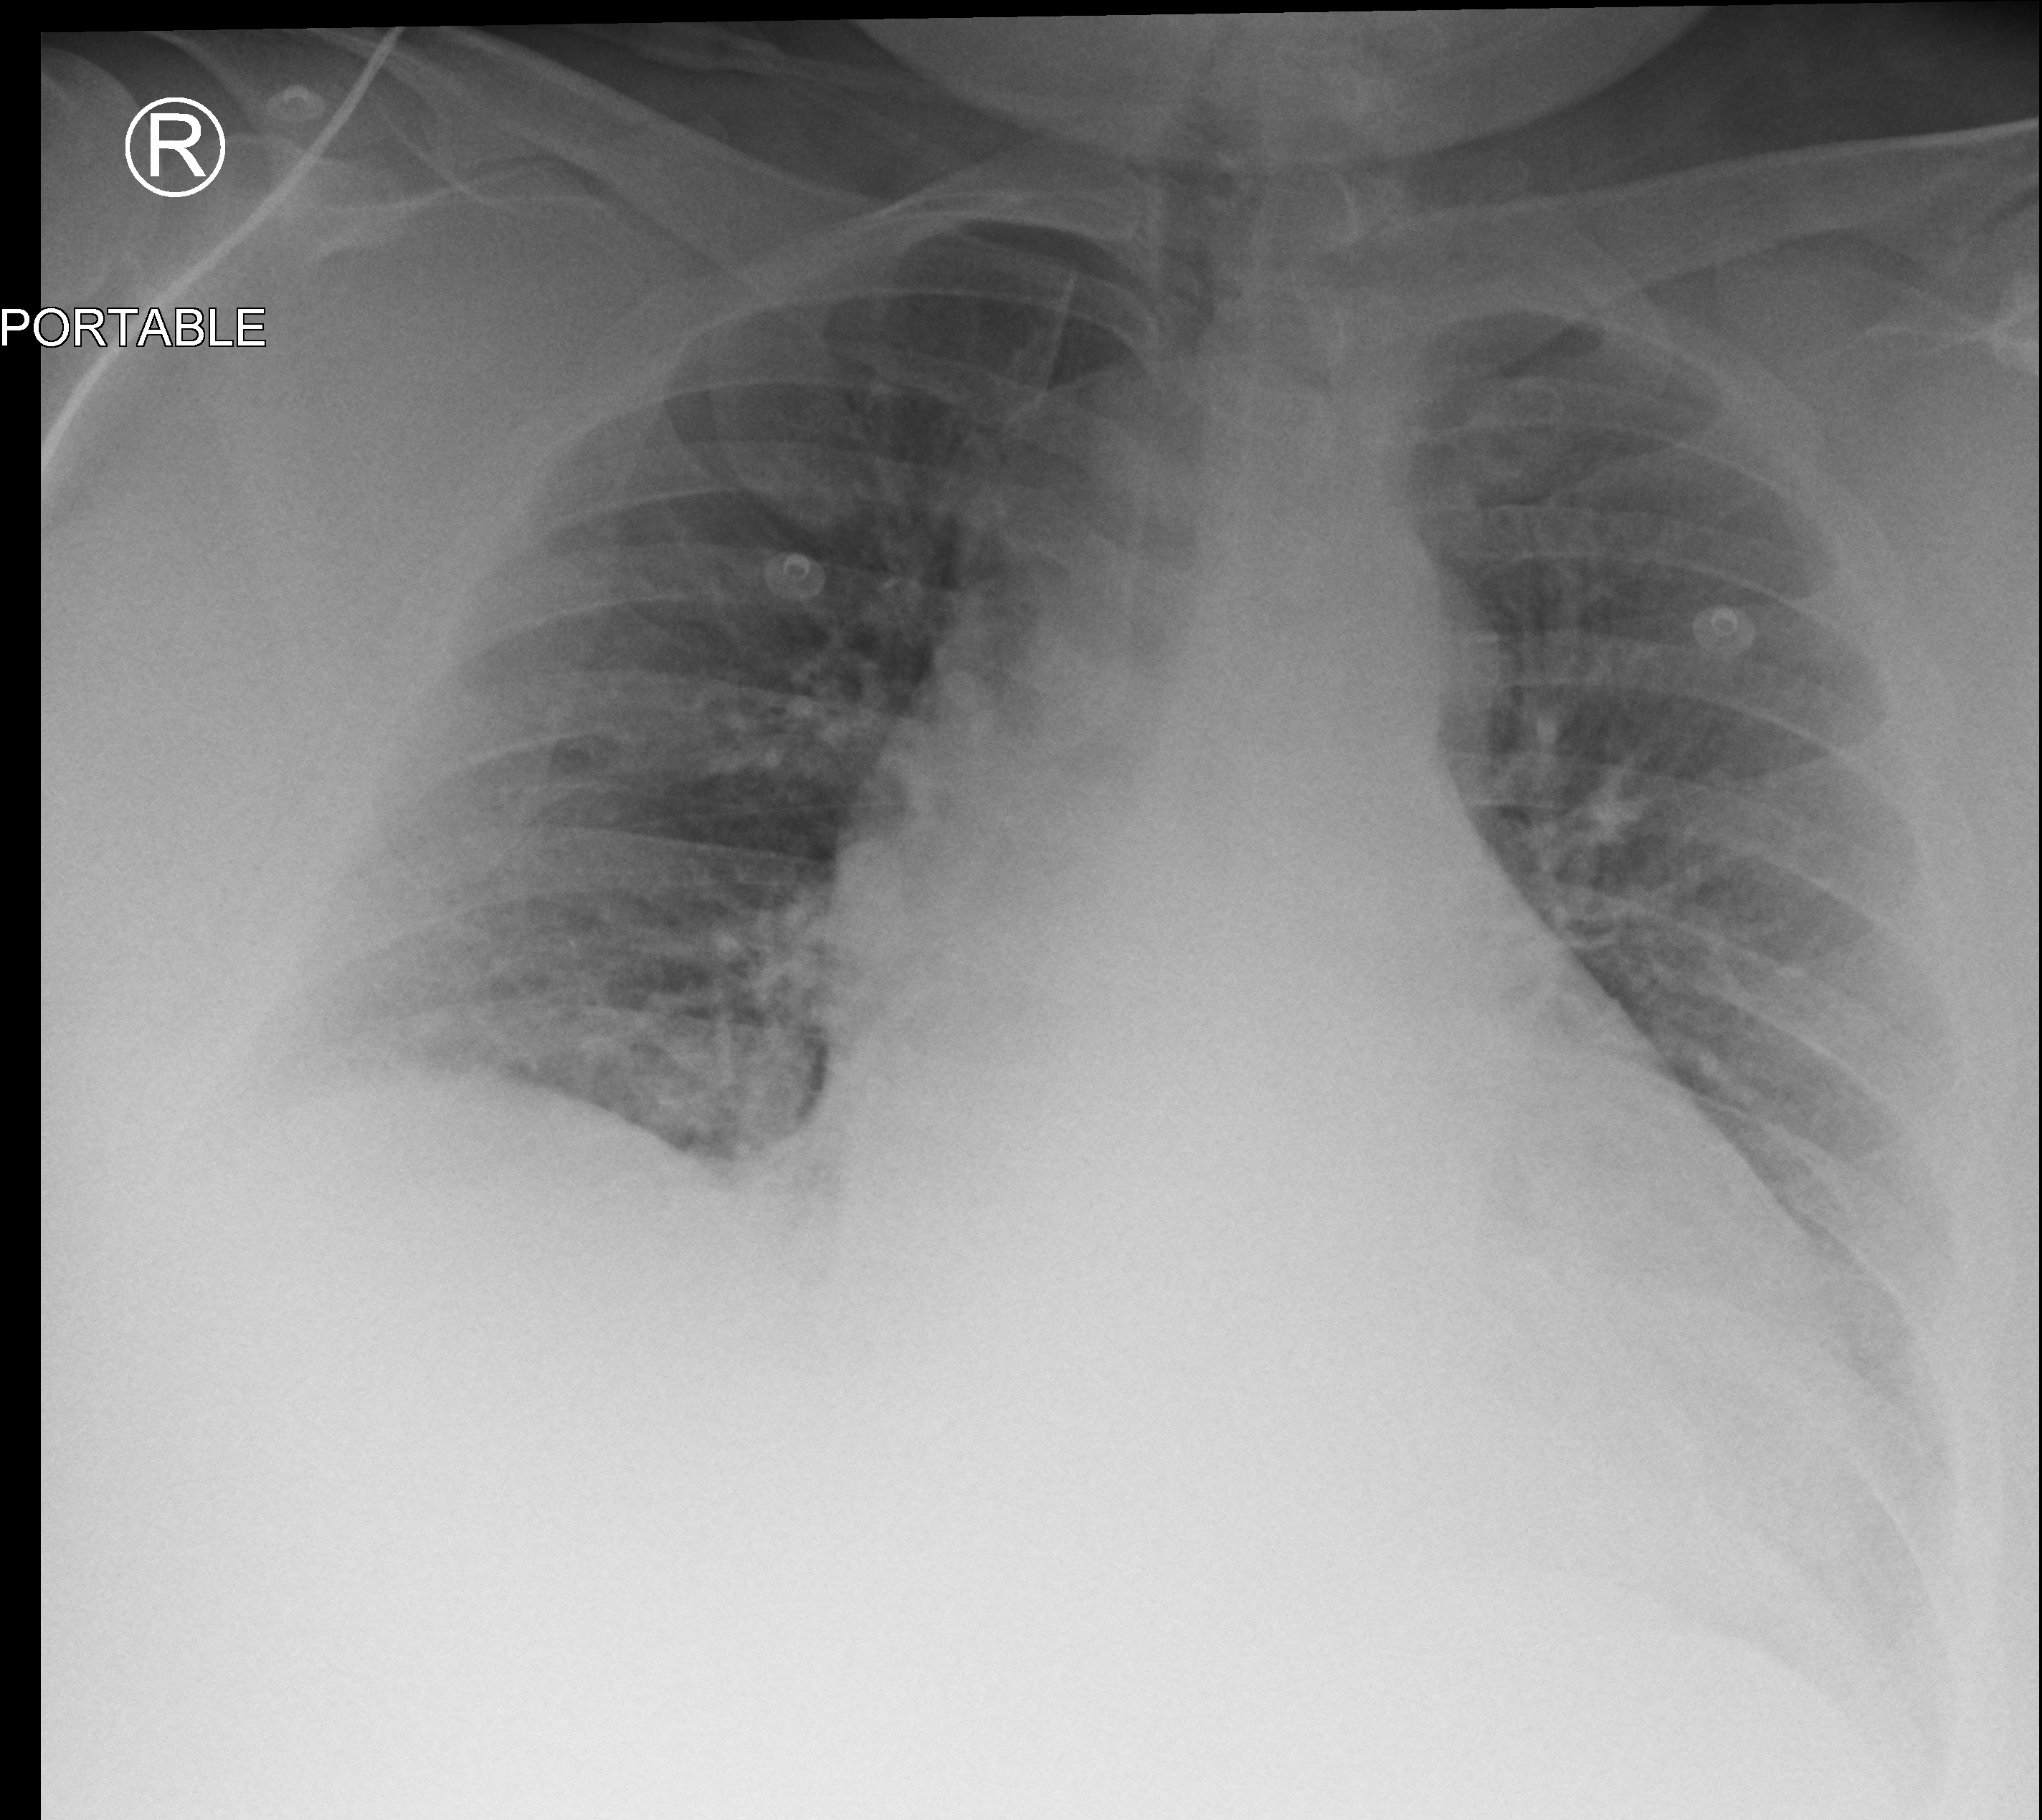
Bedside chest radiograph (computed radiography), anteroposterior (AP) projection. Patient hospitalised with COVID-19; male, aged 18–59 years.
Hospital-stay facts (about this admission, not read from this image; timing relative to this image not recorded): COPD (admission record): no; admitted to intensive care during this hospital stay: no; mechanically ventilated during this hospital stay: no.